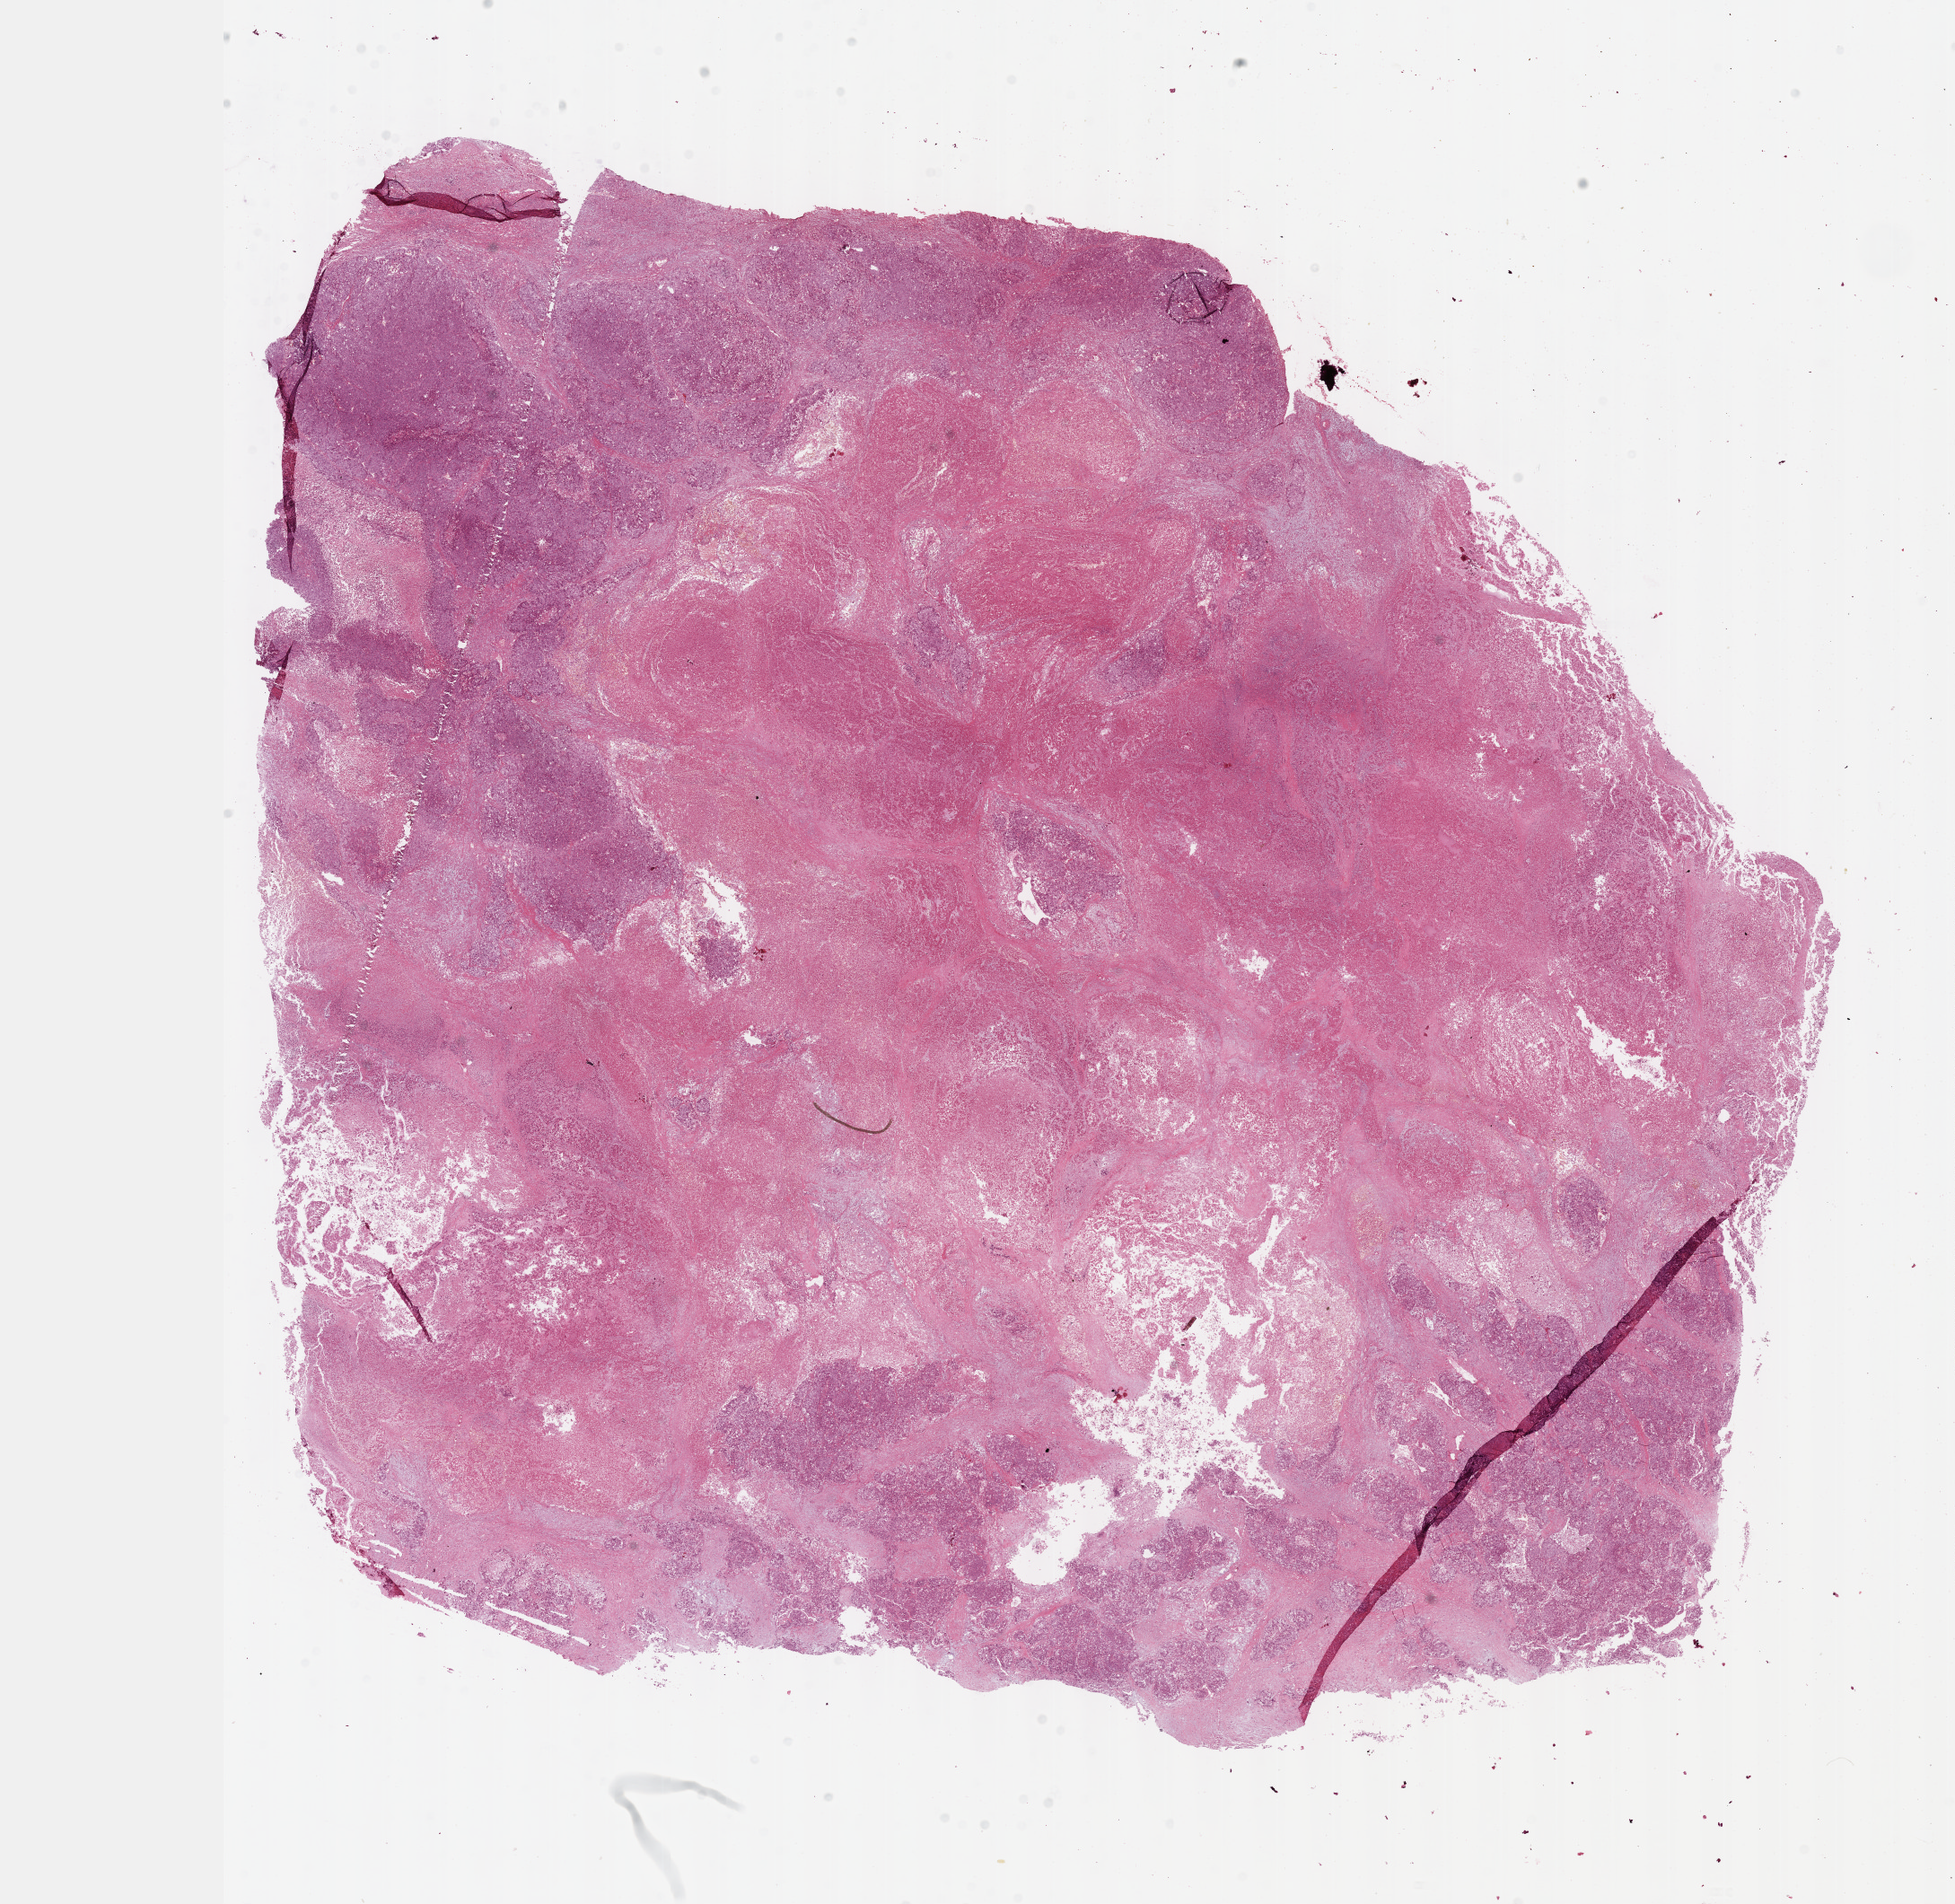
H&E-stained whole-slide image, low-resolution overview of the scanned area, about 17.6 x 17.1 mm. Formalin-fixed paraffin-embedded (FFPE) diagnostic section. Sample: primary tumour, liver. Male, age 54 years at initial diagnosis. Histologic grade: G3 (poorly differentiated).
* histologic diagnosis: Hepatocellular carcinoma, NOS
* AJCC pathologic stage: IIIA